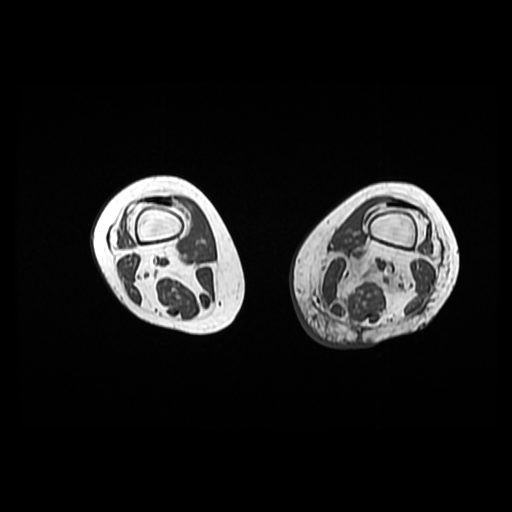
MRI of an extremity soft-tissue mass, one axial slice; slice 17 of 42 in the series (ordered by position); 6 mm slice thickness; 512 × 512 image matrix, field of view 420 × 420 mm. Female patient. From the clinical record (not read from this slice): histological type: pleomorphic leiomyosarcoma; grade: high; site of the primary tumour: left thigh.
Annotated regions visible in this slice (expert manual segmentation):
- gross tumour volume including surrounding oedema: box from (x=313, y=249) to (x=412, y=321) px